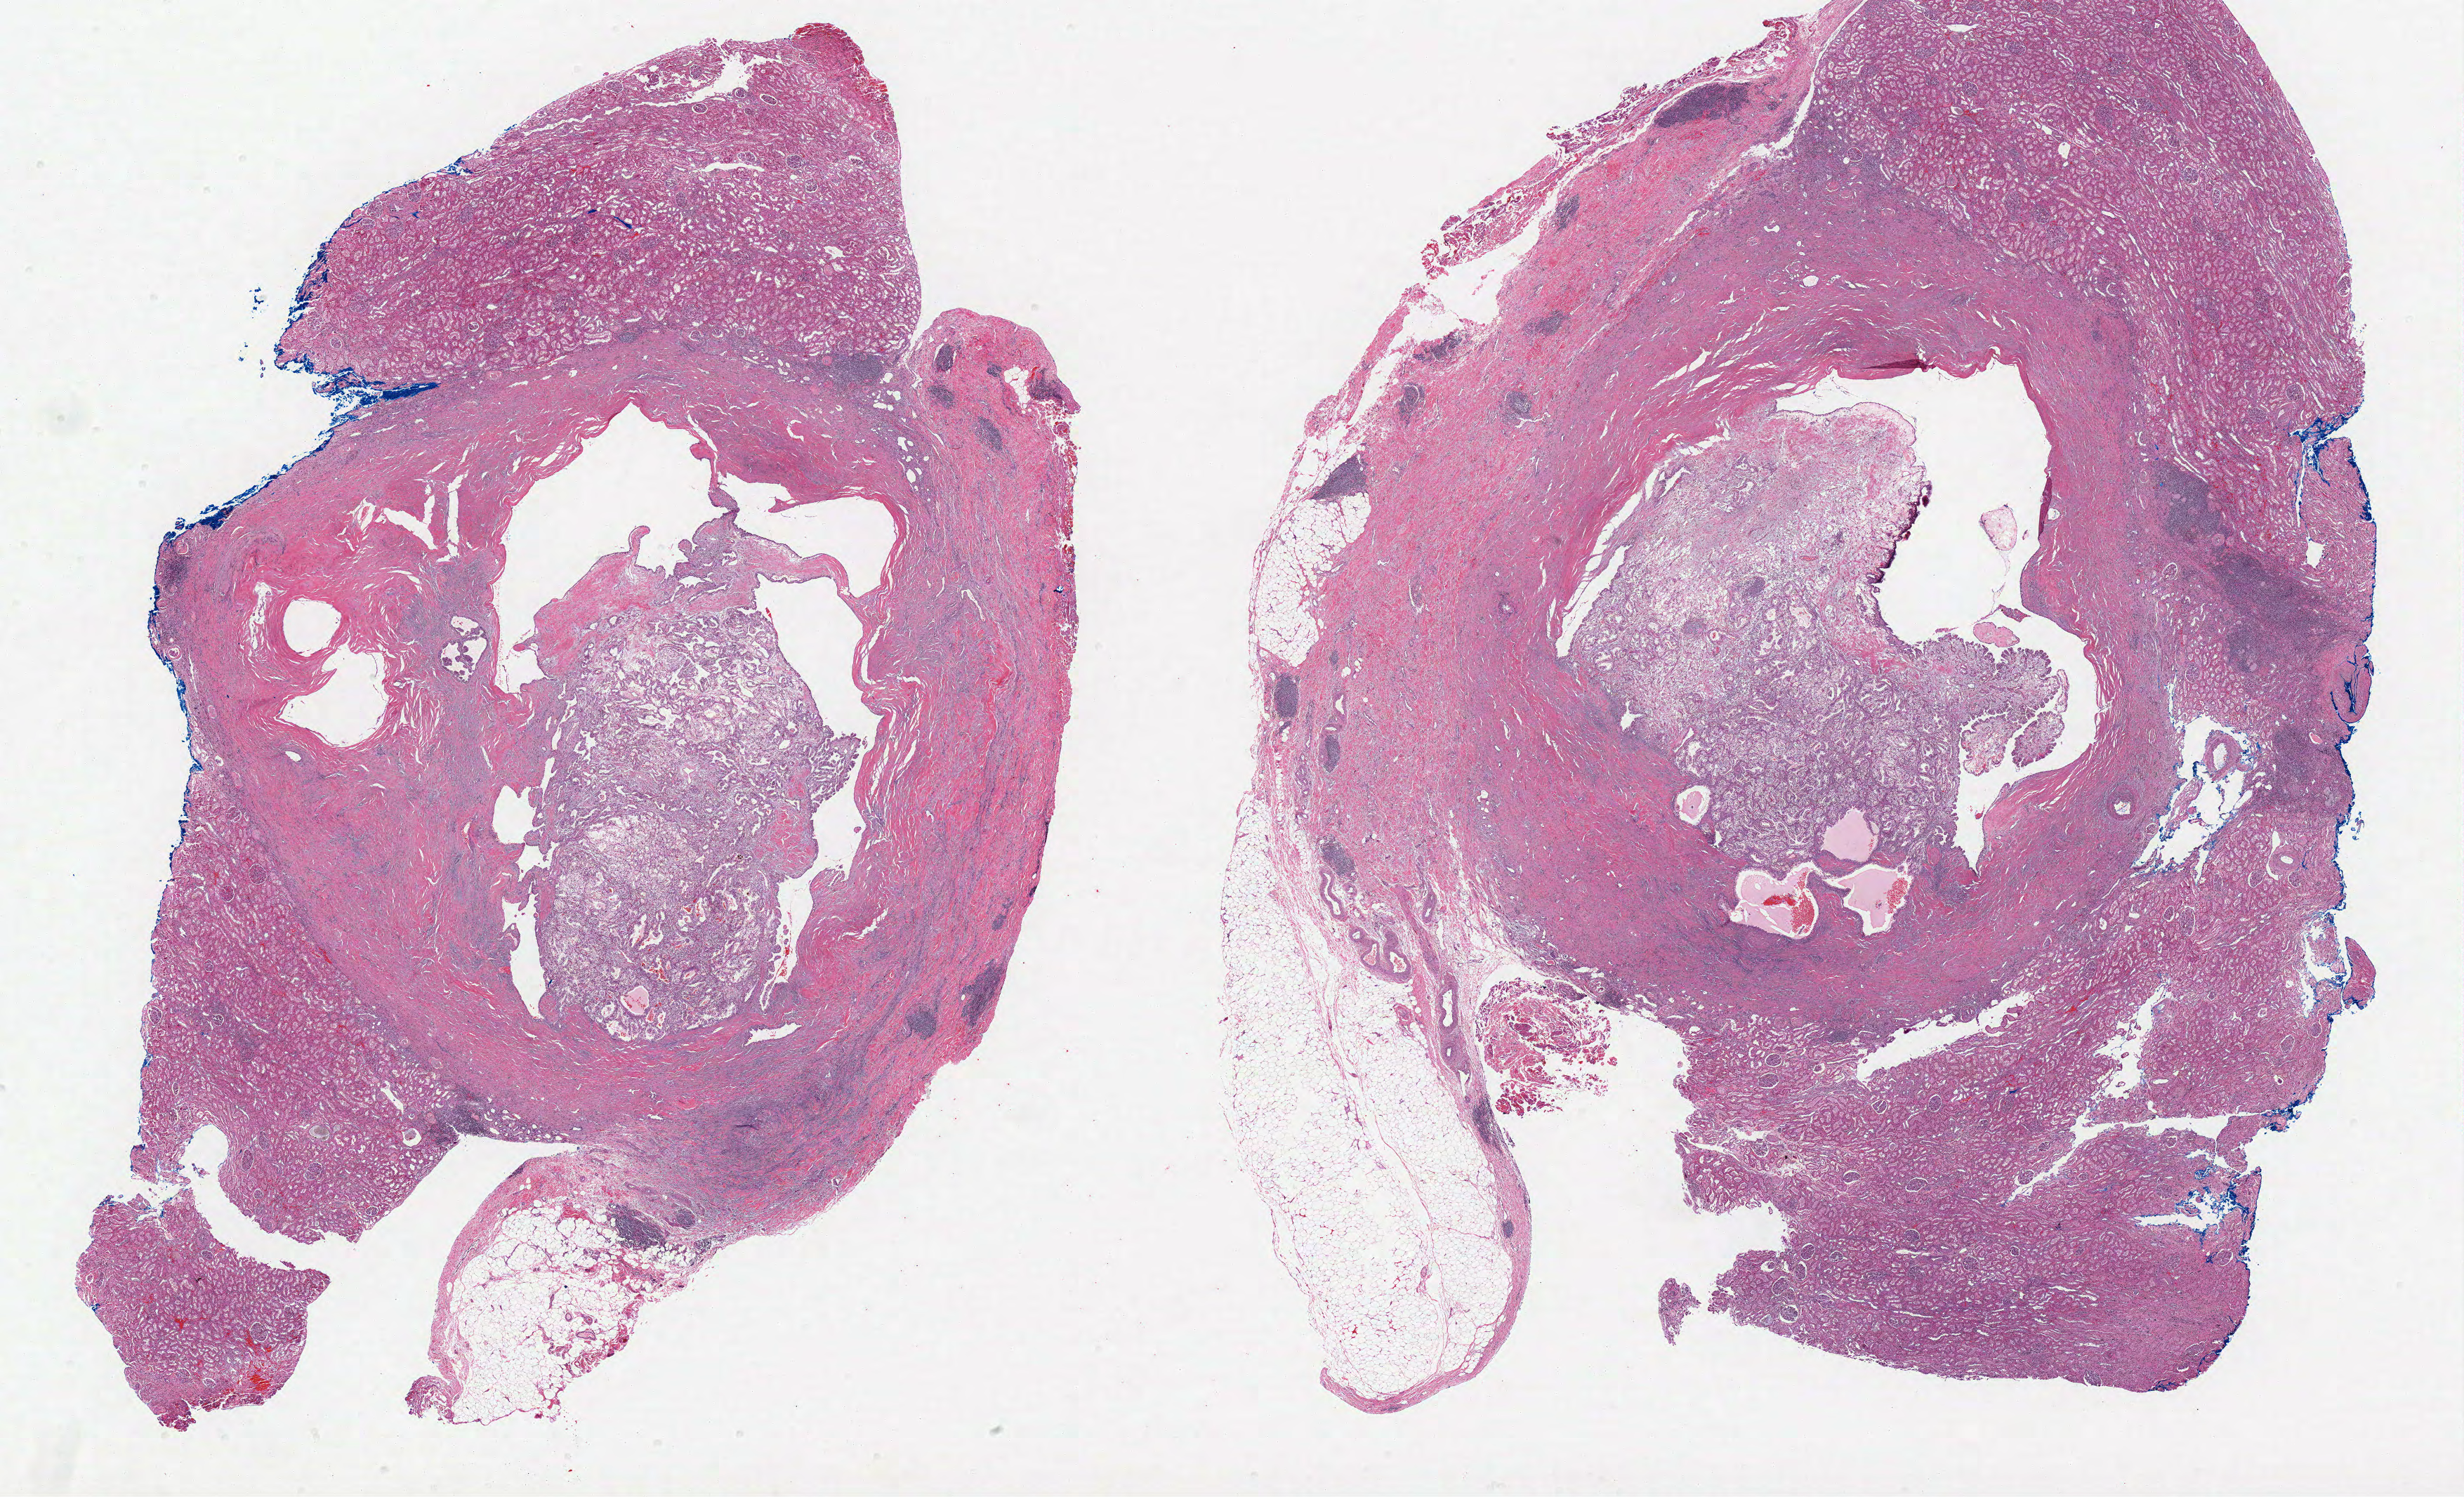
Digitized H&E tissue section (whole slide), low-resolution overview of the scanned area, about 28.1 x 17.0 mm; formalin-fixed paraffin-embedded (FFPE) diagnostic section; kidney, primary tumour sample. Female, age 67 years at initial diagnosis. Histologic grade: G2 (moderately differentiated).
AJCC pathologic stage: I. Diagnosis: Clear cell adenocarcinoma, NOS.